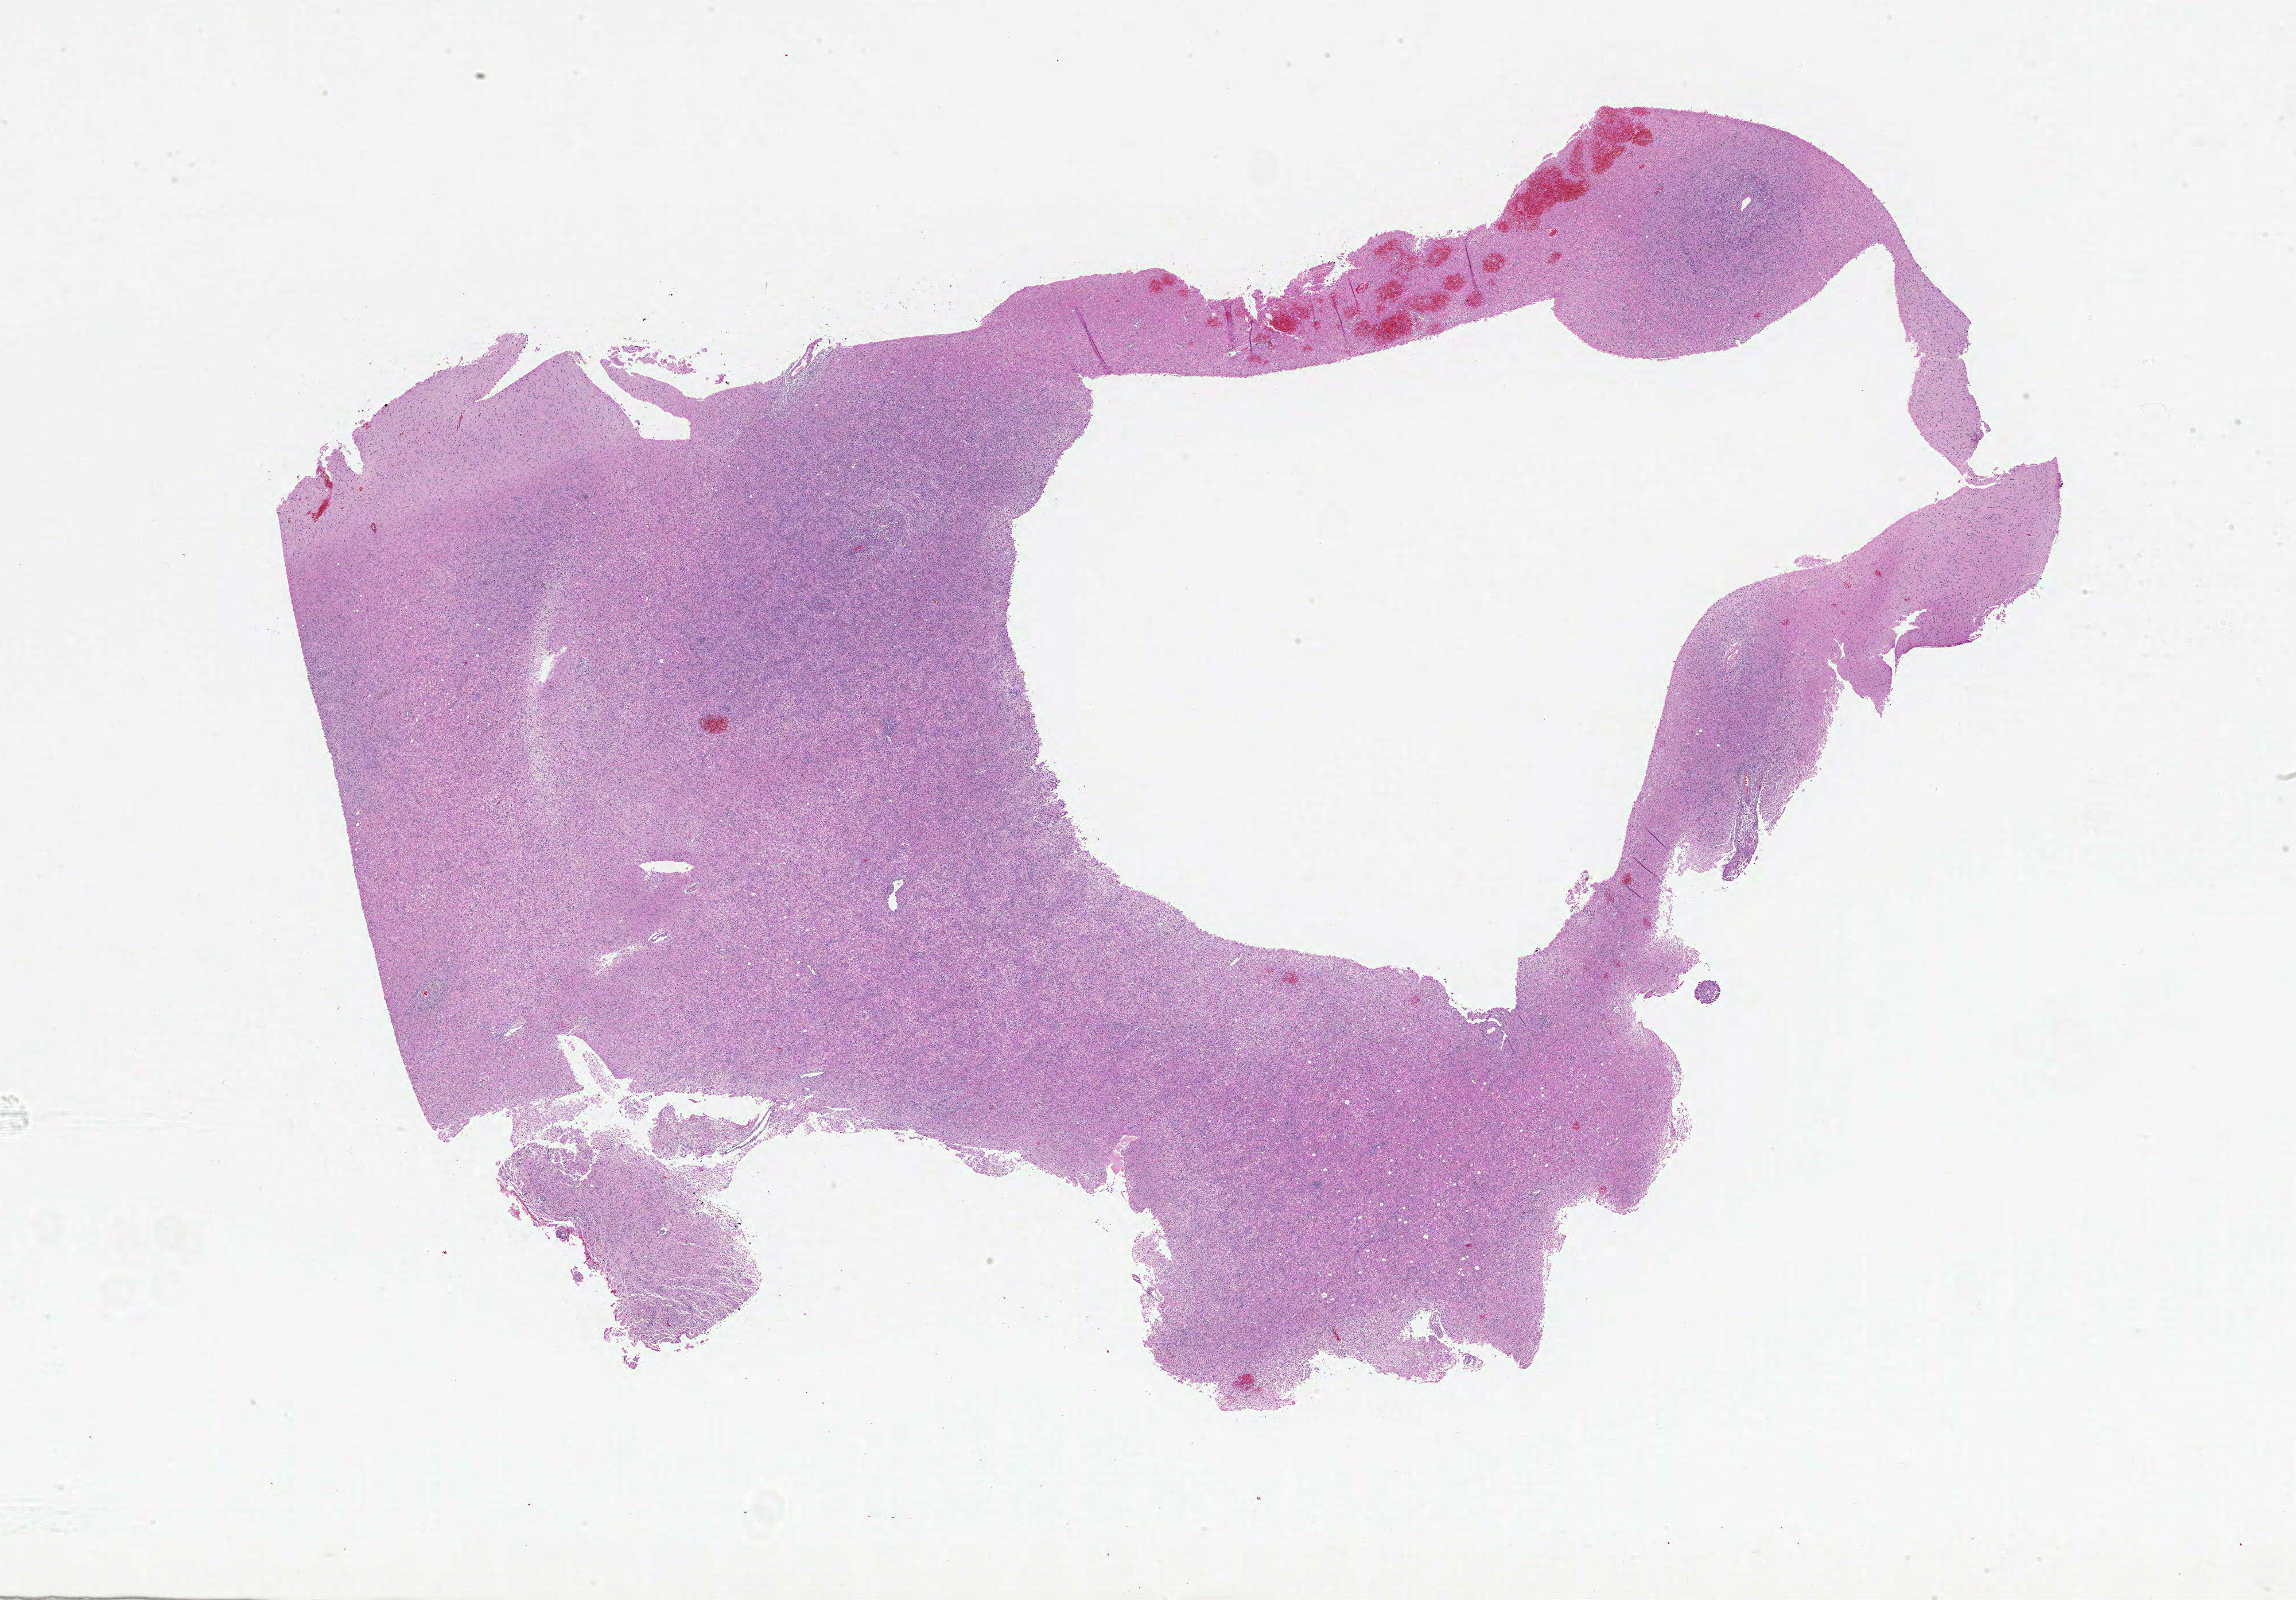
Digitized H&E tissue section (whole slide) — whole scanned area (about 32.0 x 22.3 mm, acquisition: 20x scan) shown as a low-resolution overview, formalin-fixed paraffin-embedded (FFPE) diagnostic section, sample: primary tumour, brain. Female patient; age at initial diagnosis 65 years.
- pathologic diagnosis: Glioblastoma